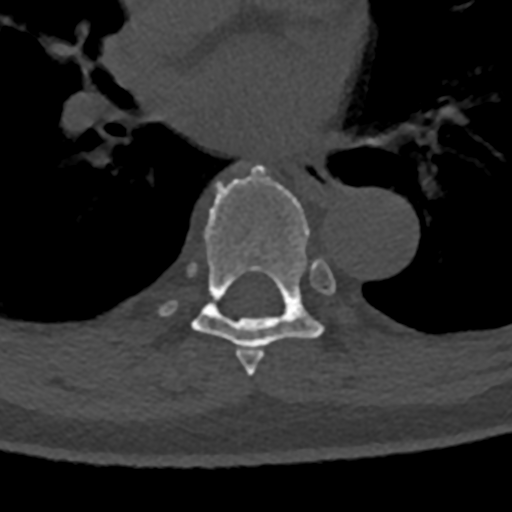
CT including the spine, one axial slice. Position 765 of 797 along the scan axis. 120 kVp. Bone window (W 1800 / L 400 HU). 0.5 mm slice thickness. 512 × 512 image matrix, field of view 160 × 160 mm. Male patient, age 74 years. From the clinical record (not read from this slice): primary cancer: renal; vertebrae with lytic lesions (as recorded): T10, L1, L2, L3, L4, L5.
Outlined on this slice (semi-automatically segmented with operator editing):
- T6 vertebra: bounding box [x1, y1, x2, y2] px = [245, 351, 264, 376]
- T7 vertebra: [157, 165, 348, 367]